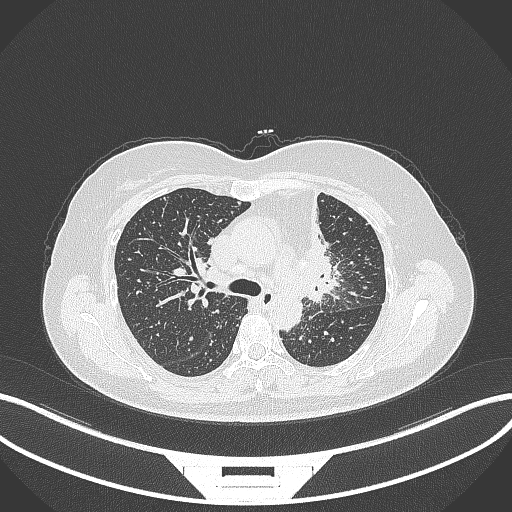
Chest CT, one axial slice. 120 kVp. Lung window (W 1500 / L -600 HU). 1 mm slice thickness. 512 × 512 image matrix. Female patient, age 49 years. From the clinical record (not read from this slice): clinical TNM (as recorded): T1c N0 M1.
Annotated regions visible in this slice (bounding box drawn by a radiologist):
- lung tumour (recorded histology: adenocarcinoma): bounding box [x1, y1, x2, y2] px = [288, 190, 346, 308]